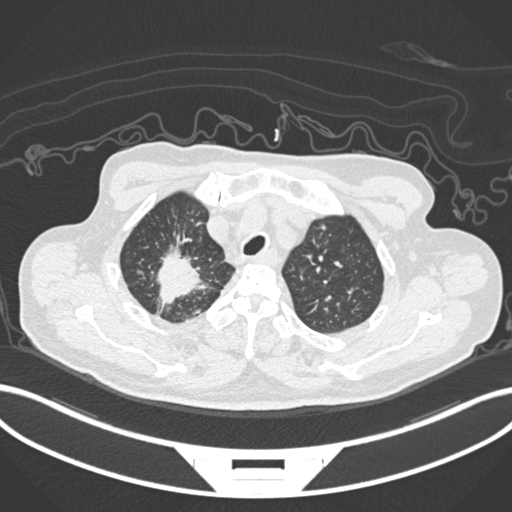
Chest CT, one axial slice; reconstruction kernel B30f; 120 kVp; lung window (W 1500 / L -600 HU); 1 mm slice thickness; 512 × 512 image matrix. Patient: male, 69 years. From the clinical record (not read from this slice): clinical TNM (as recorded): T1c N1 M1.
Annotated regions visible in this slice (rectangle marked by the reading radiologist):
- lung tumour (recorded histology: adenocarcinoma): box from (x=151, y=243) to (x=210, y=309) px